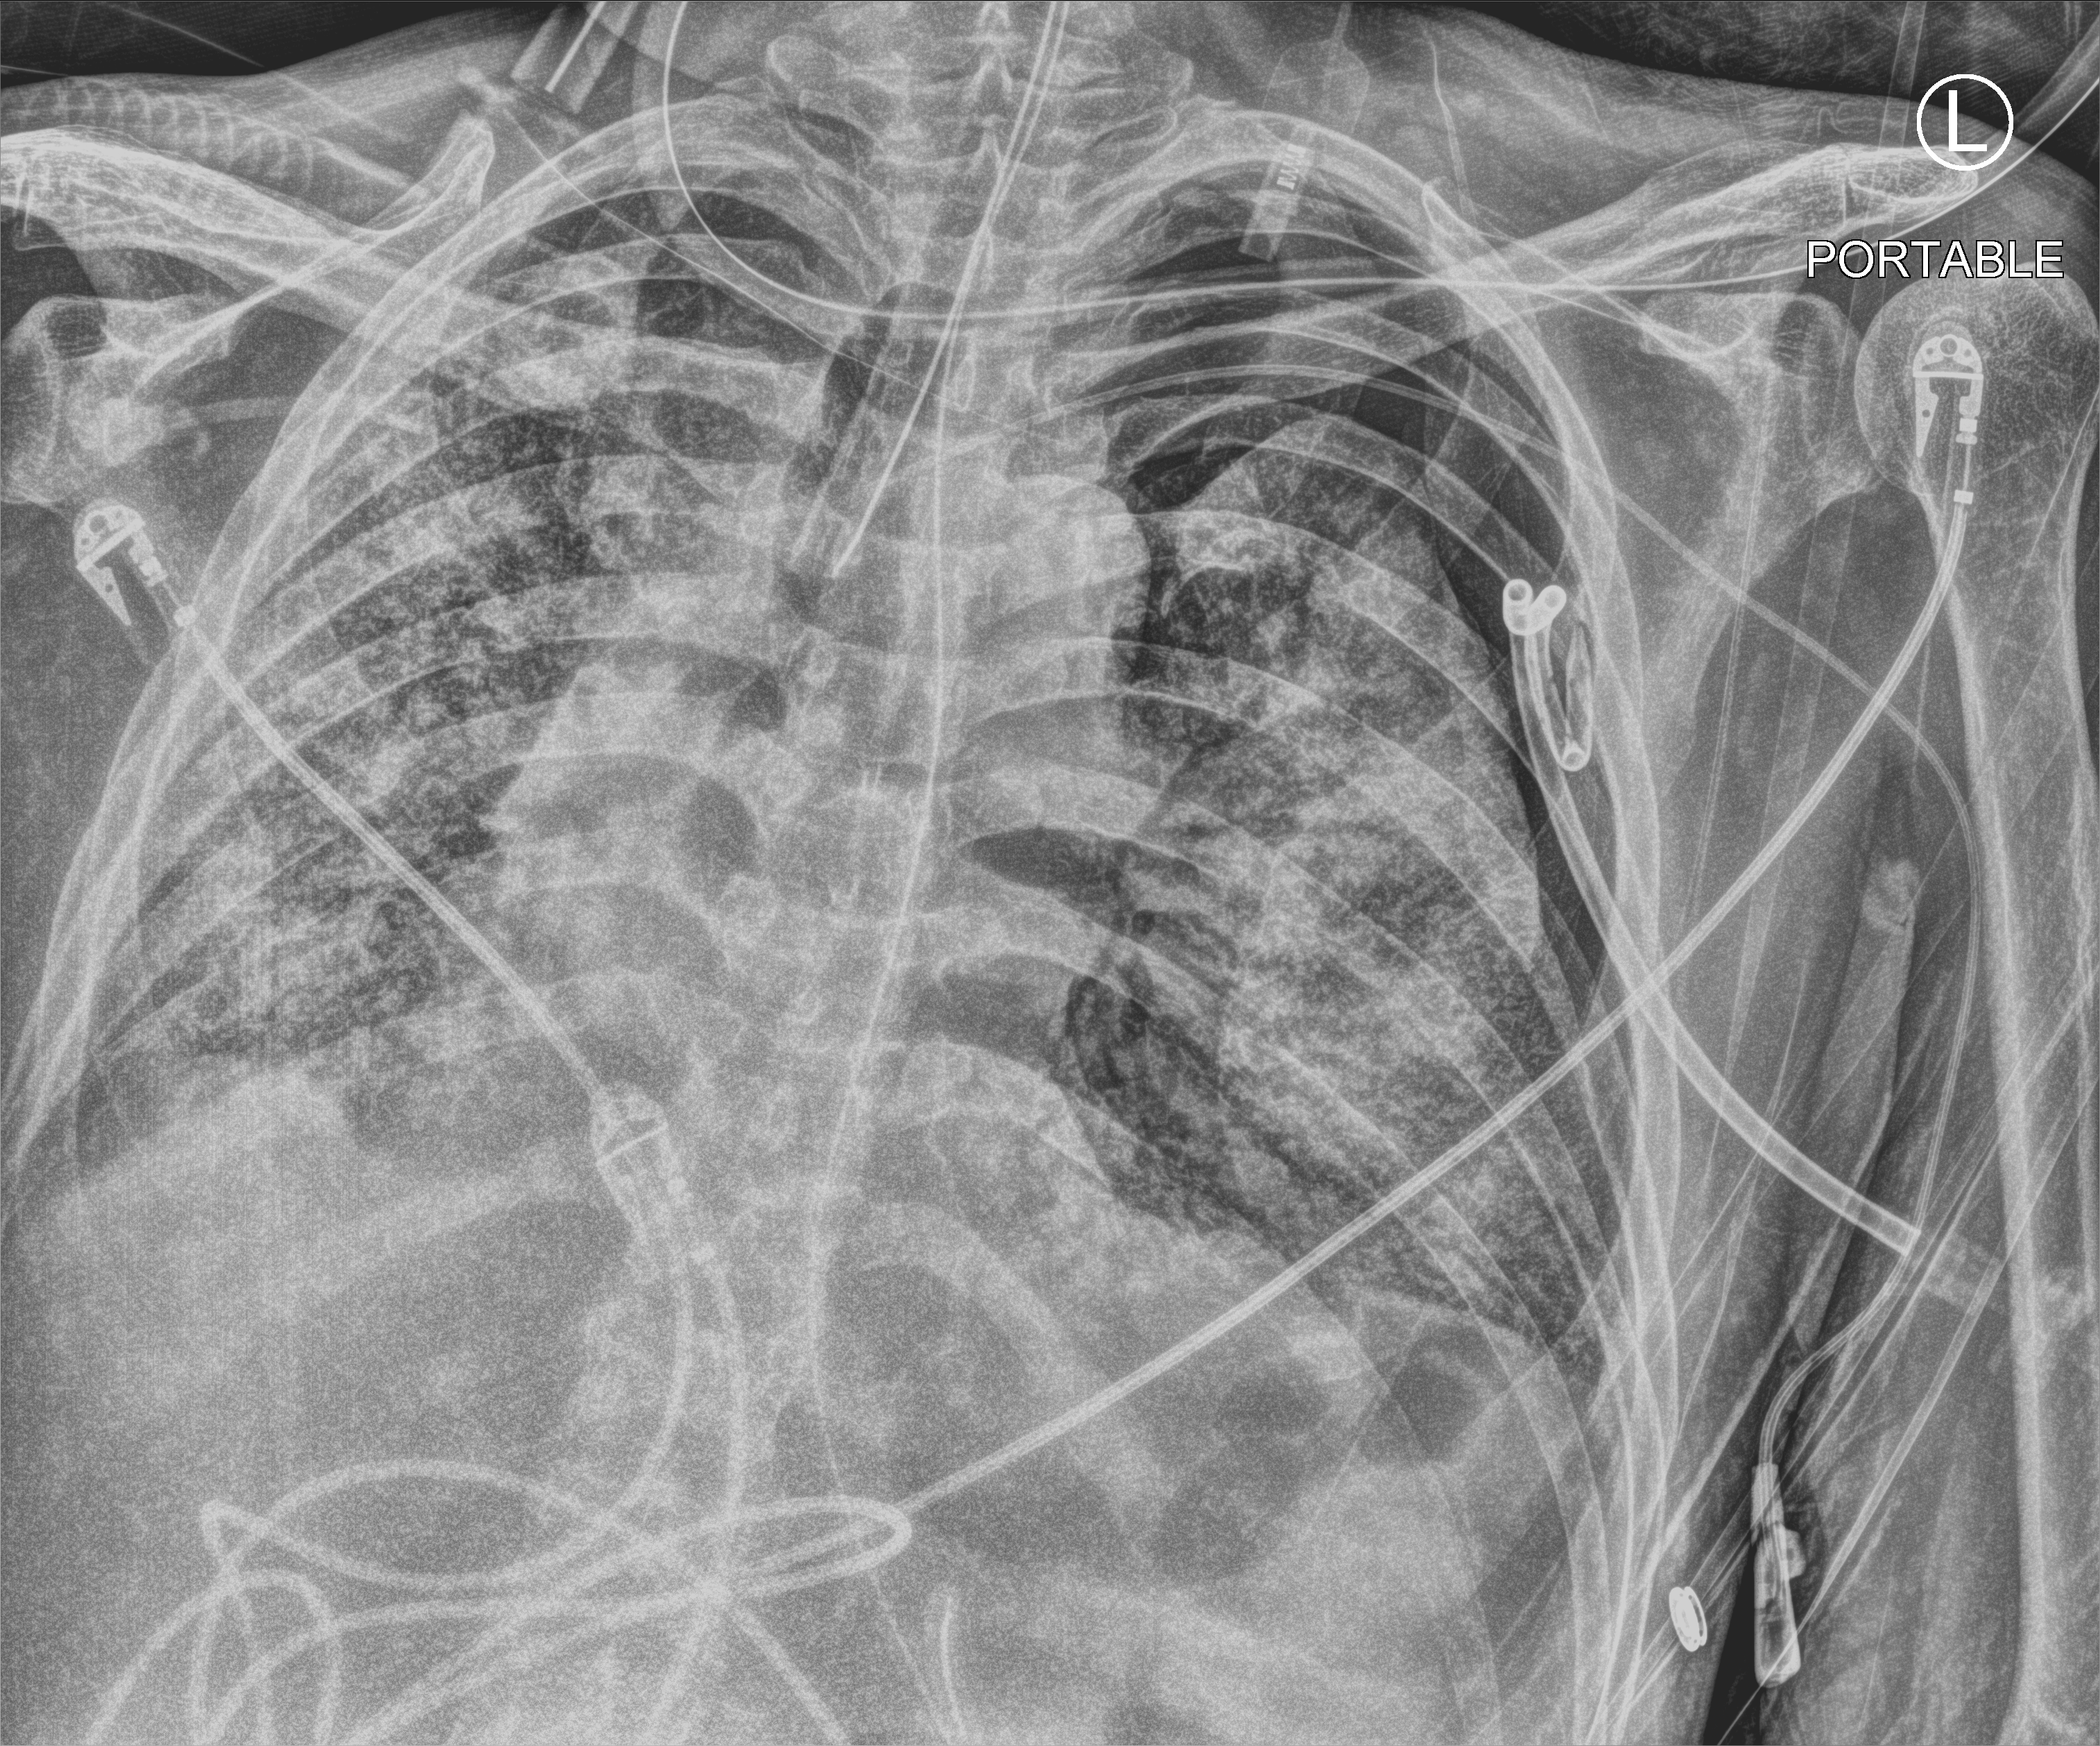
Portable chest radiograph, anteroposterior (AP) projection. Male patient hospitalised with COVID-19, age 60–74 years.
Admission-level facts for this patient (not findings on this image; timing relative to this image not recorded): admitted to intensive care during this hospital stay: yes.